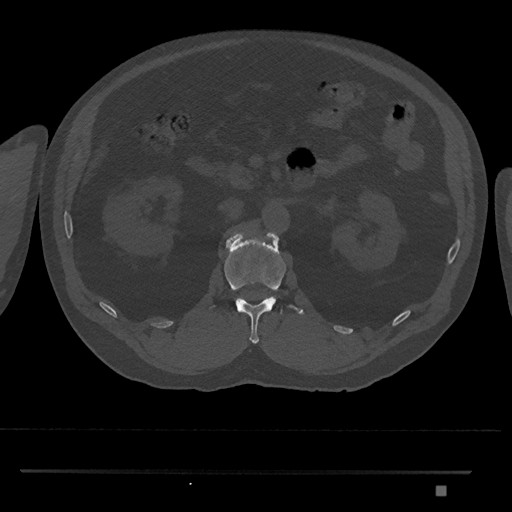
CT including the spine, one axial slice; position 812 of 1134 along the scan axis; 120 kVp; bone window (W 1800 / L 400 HU); 0.5 mm slice thickness; 512 × 512 image matrix, field of view 429 × 429 mm. Male patient, age 65 years. Case-level facts recorded for this patient, not image findings: primary cancer: prostate.
Structures marked on this image (semi-automatic segmentation, software-assisted and operator-edited):
- L1 vertebra: box from (x=209, y=231) to (x=304, y=344) px